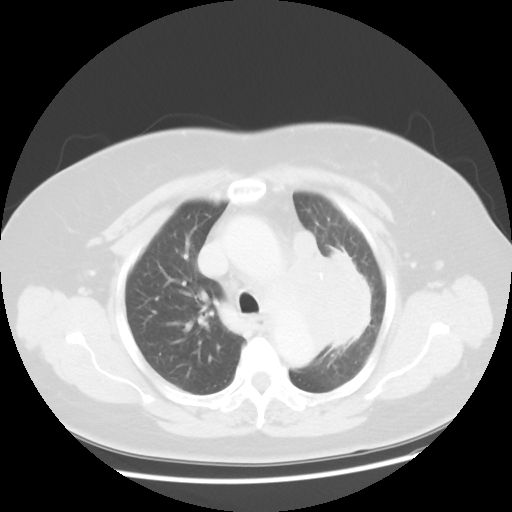
Chest CT, one axial slice; position 34 of 49 along the scan axis; reconstruction kernel STANDARD; lung window (W 1500 / L -600 HU); 512 × 512 image matrix, field of view 374 × 374 mm. Female patient, age 58 years. Case-level facts recorded for this patient, not image findings: clinical TNM (as recorded): T4 N3 M0; histopathological grade: G3.
Annotated regions visible in this slice (bounding box drawn by a radiologist):
- lung tumour (recorded histology: small cell carcinoma): box from (x=284, y=225) to (x=374, y=356) px